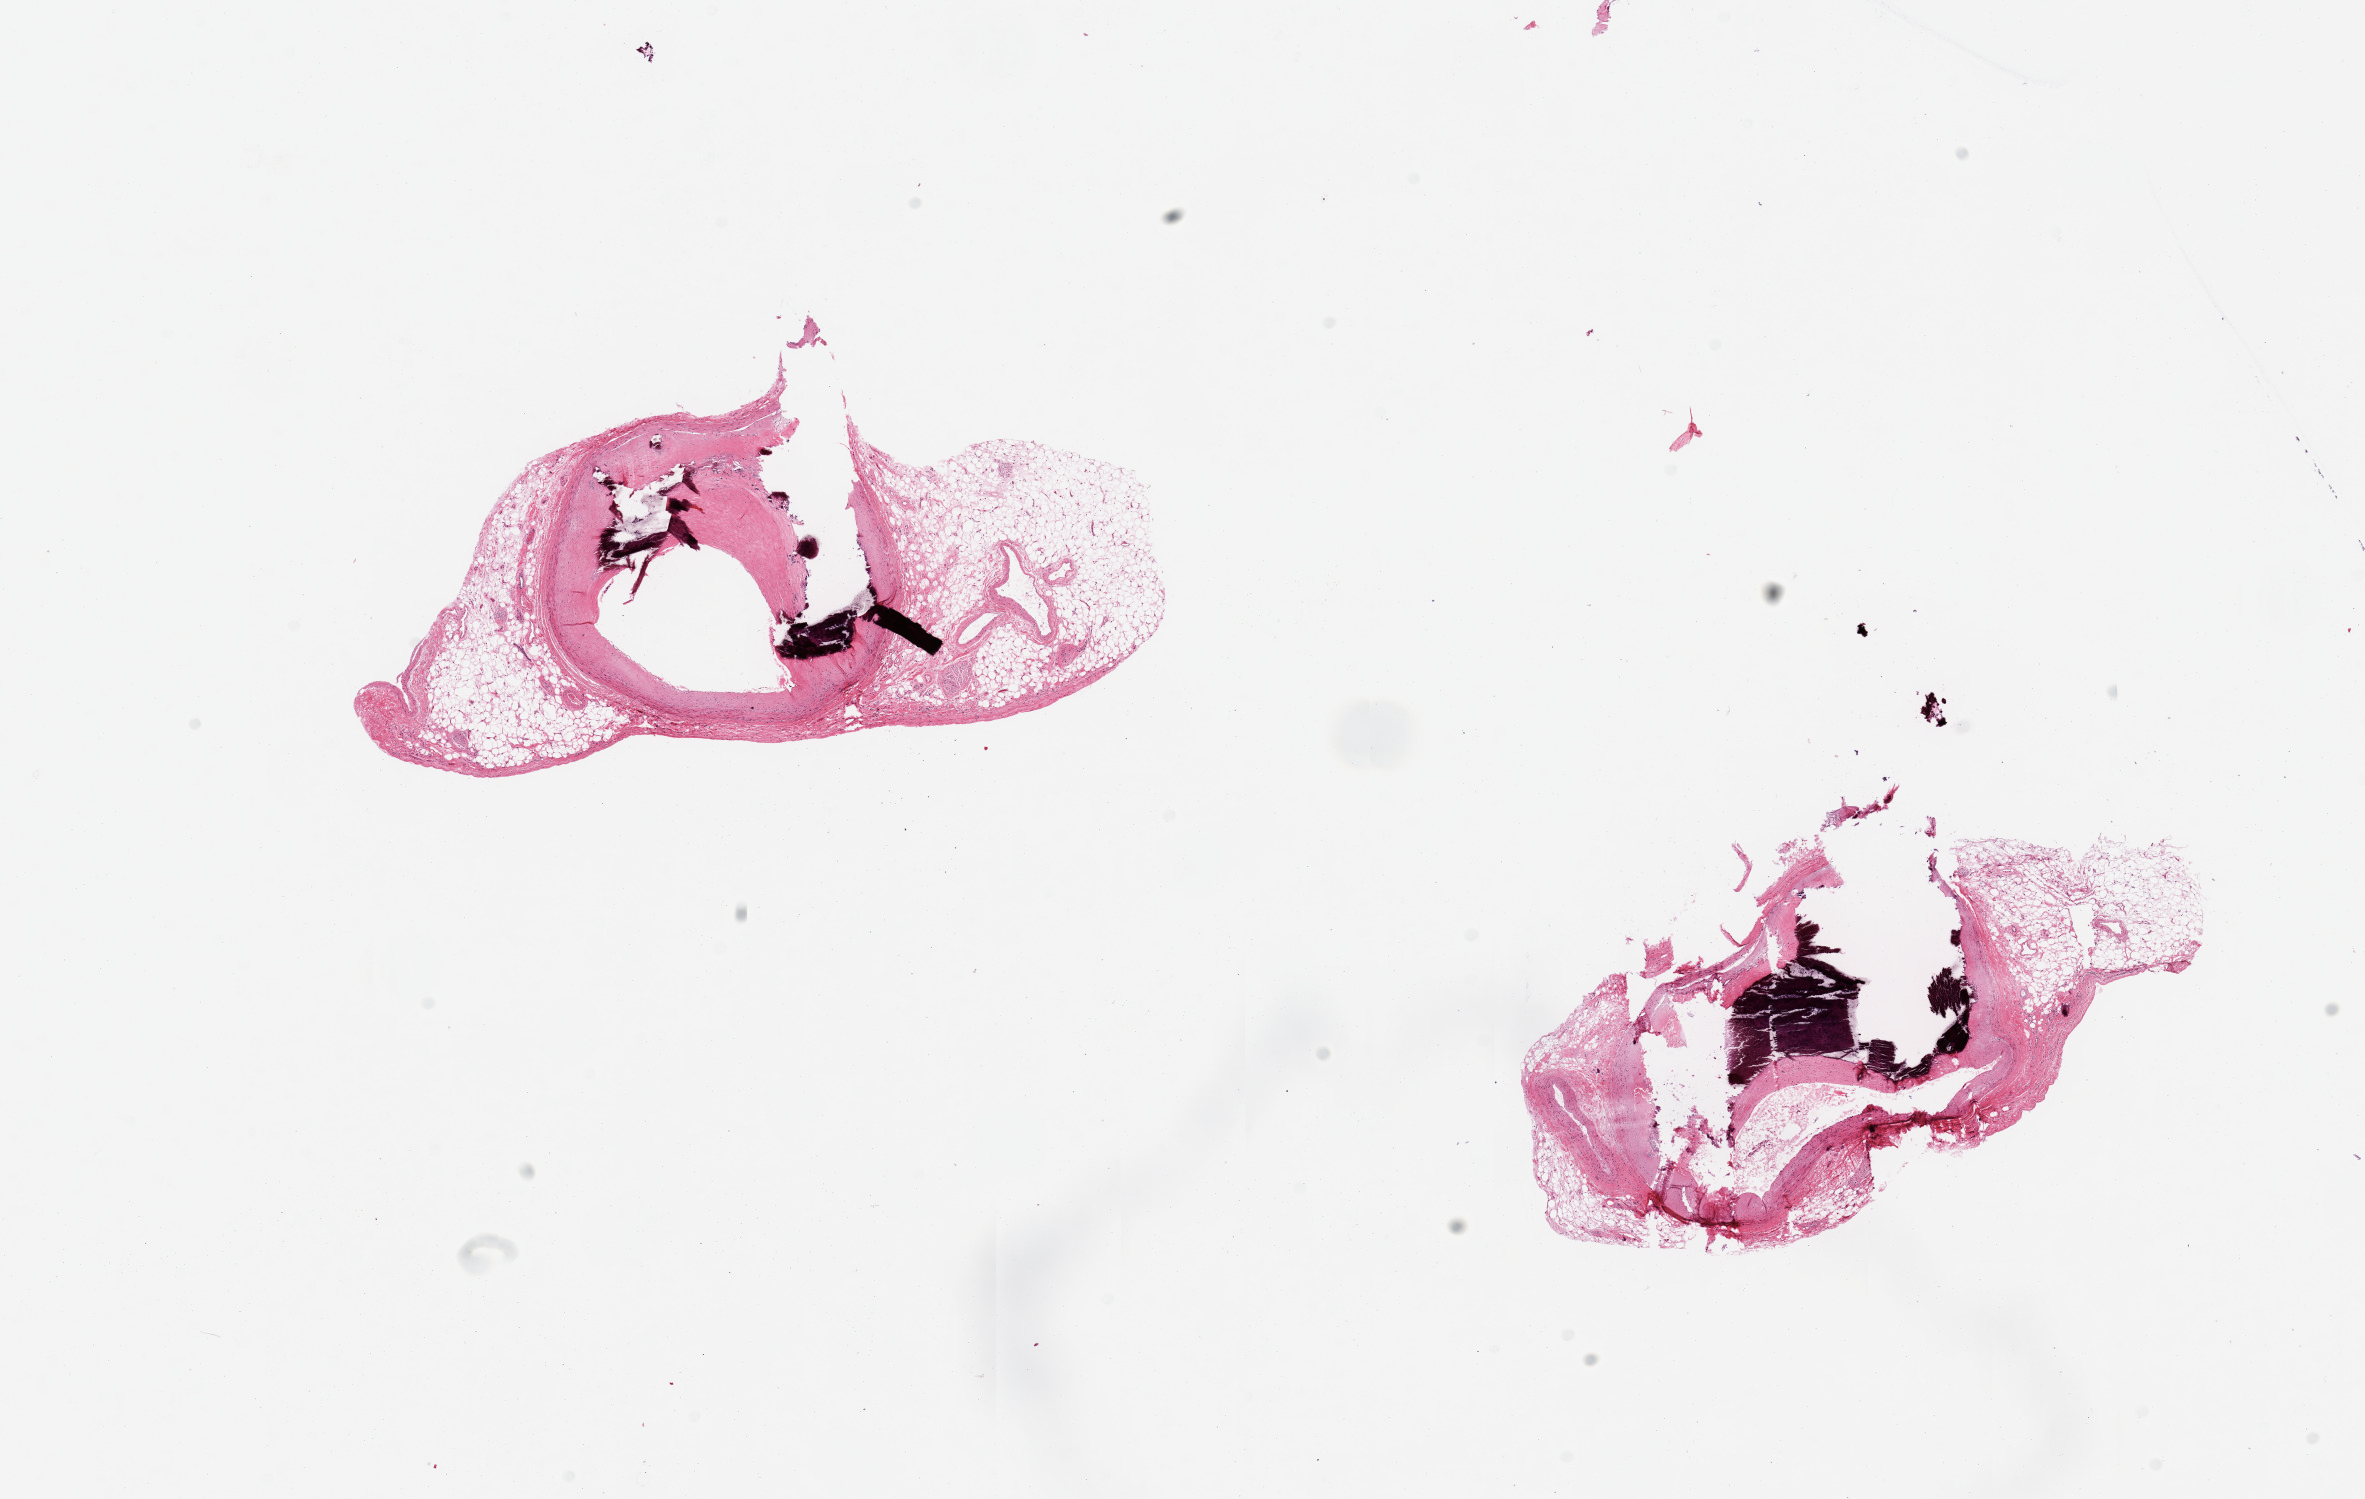
Whole-slide image, H&E stain, brightfield, low-resolution overview of the scanned area, about 18.7 x 11.9 mm; PAXgene-fixed, paraffin-embedded tissue; sampled site (target tissue): coronary artery; tissue donor sample. Donor: male.
Reviewer comment on this tissue sample: 2 pieces; atherosclerotic plaque and medial calcification narrowing the lumen by ~50%; attached adventitia and fat, ~50% of tissue.